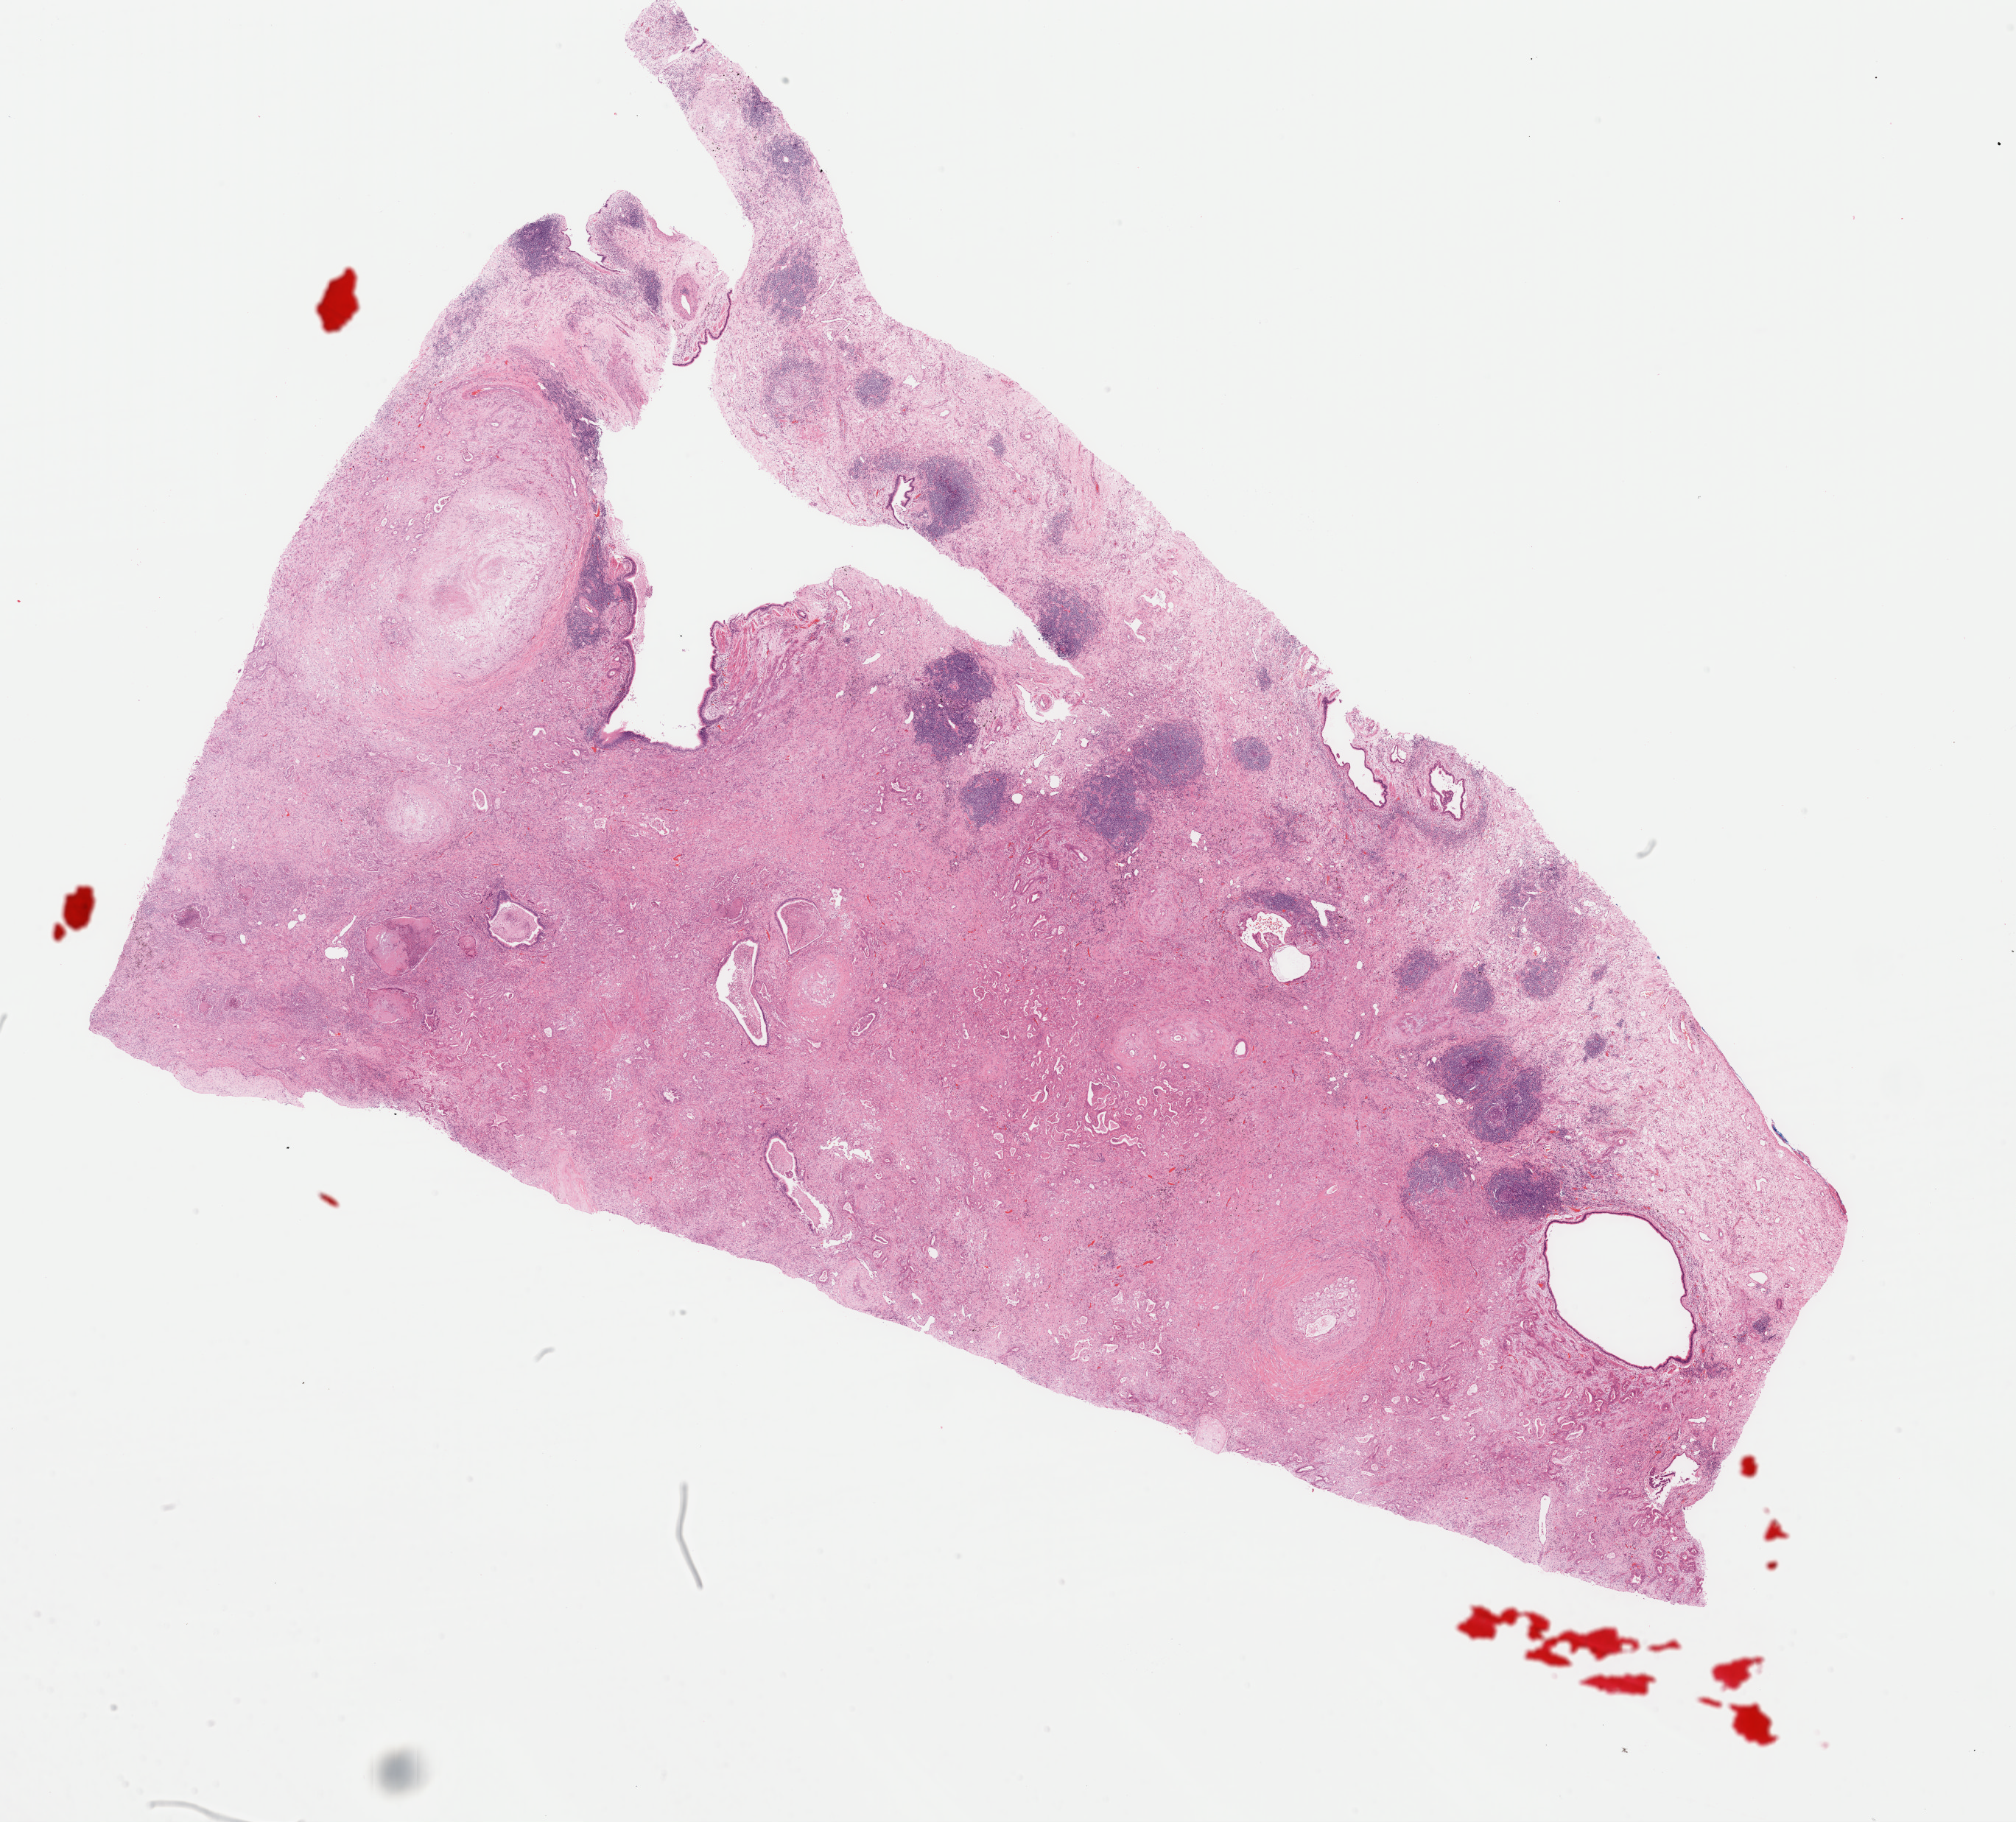
Whole-slide histology image, H&E-stained, shown as a low-resolution overview of the whole scanned area (about 21.6 x 19.5 mm, slide scanned at 40x); formalin-fixed paraffin-embedded (FFPE) diagnostic section; sample: primary tumour, bladder. Patient: male, age at initial diagnosis 66 years. Histologic grade: high grade.
* AJCC pathologic stage: II
* histologic diagnosis: Transitional cell carcinoma